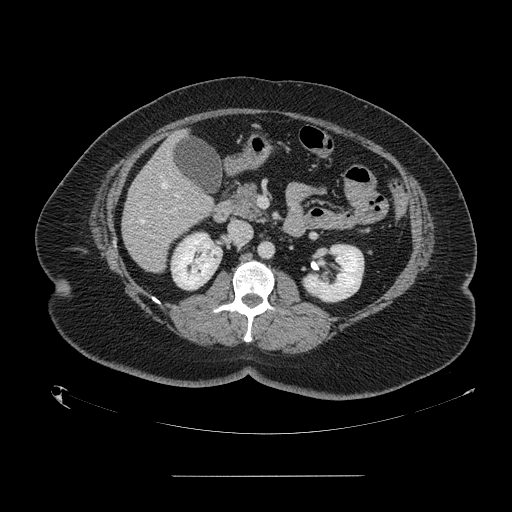
Contrast-enhanced abdominal CT, one axial slice. Position 64 of 164 along the scan axis. Intravenous contrast given. Soft-tissue window (W 400 / L 40 HU). 2.5 mm slice thickness. 512 × 512 image matrix. Female patient, age 52 years. From the clinical record (not read from this slice): diagnosis: colorectal cancer liver metastases, imaged before liver resection; multiple liver metastases: yes; largest metastasis: 3.5 cm; disease in both lobes: no.
Outlined on this slice (expert manual segmentation):
- hepatic veins: bounding box (x1, y1, x2, y2) in pixels: (140, 182, 175, 224)
- liver: (123, 134, 214, 272)
- portal vein (with intrahepatic branches): (175, 194, 178, 197)